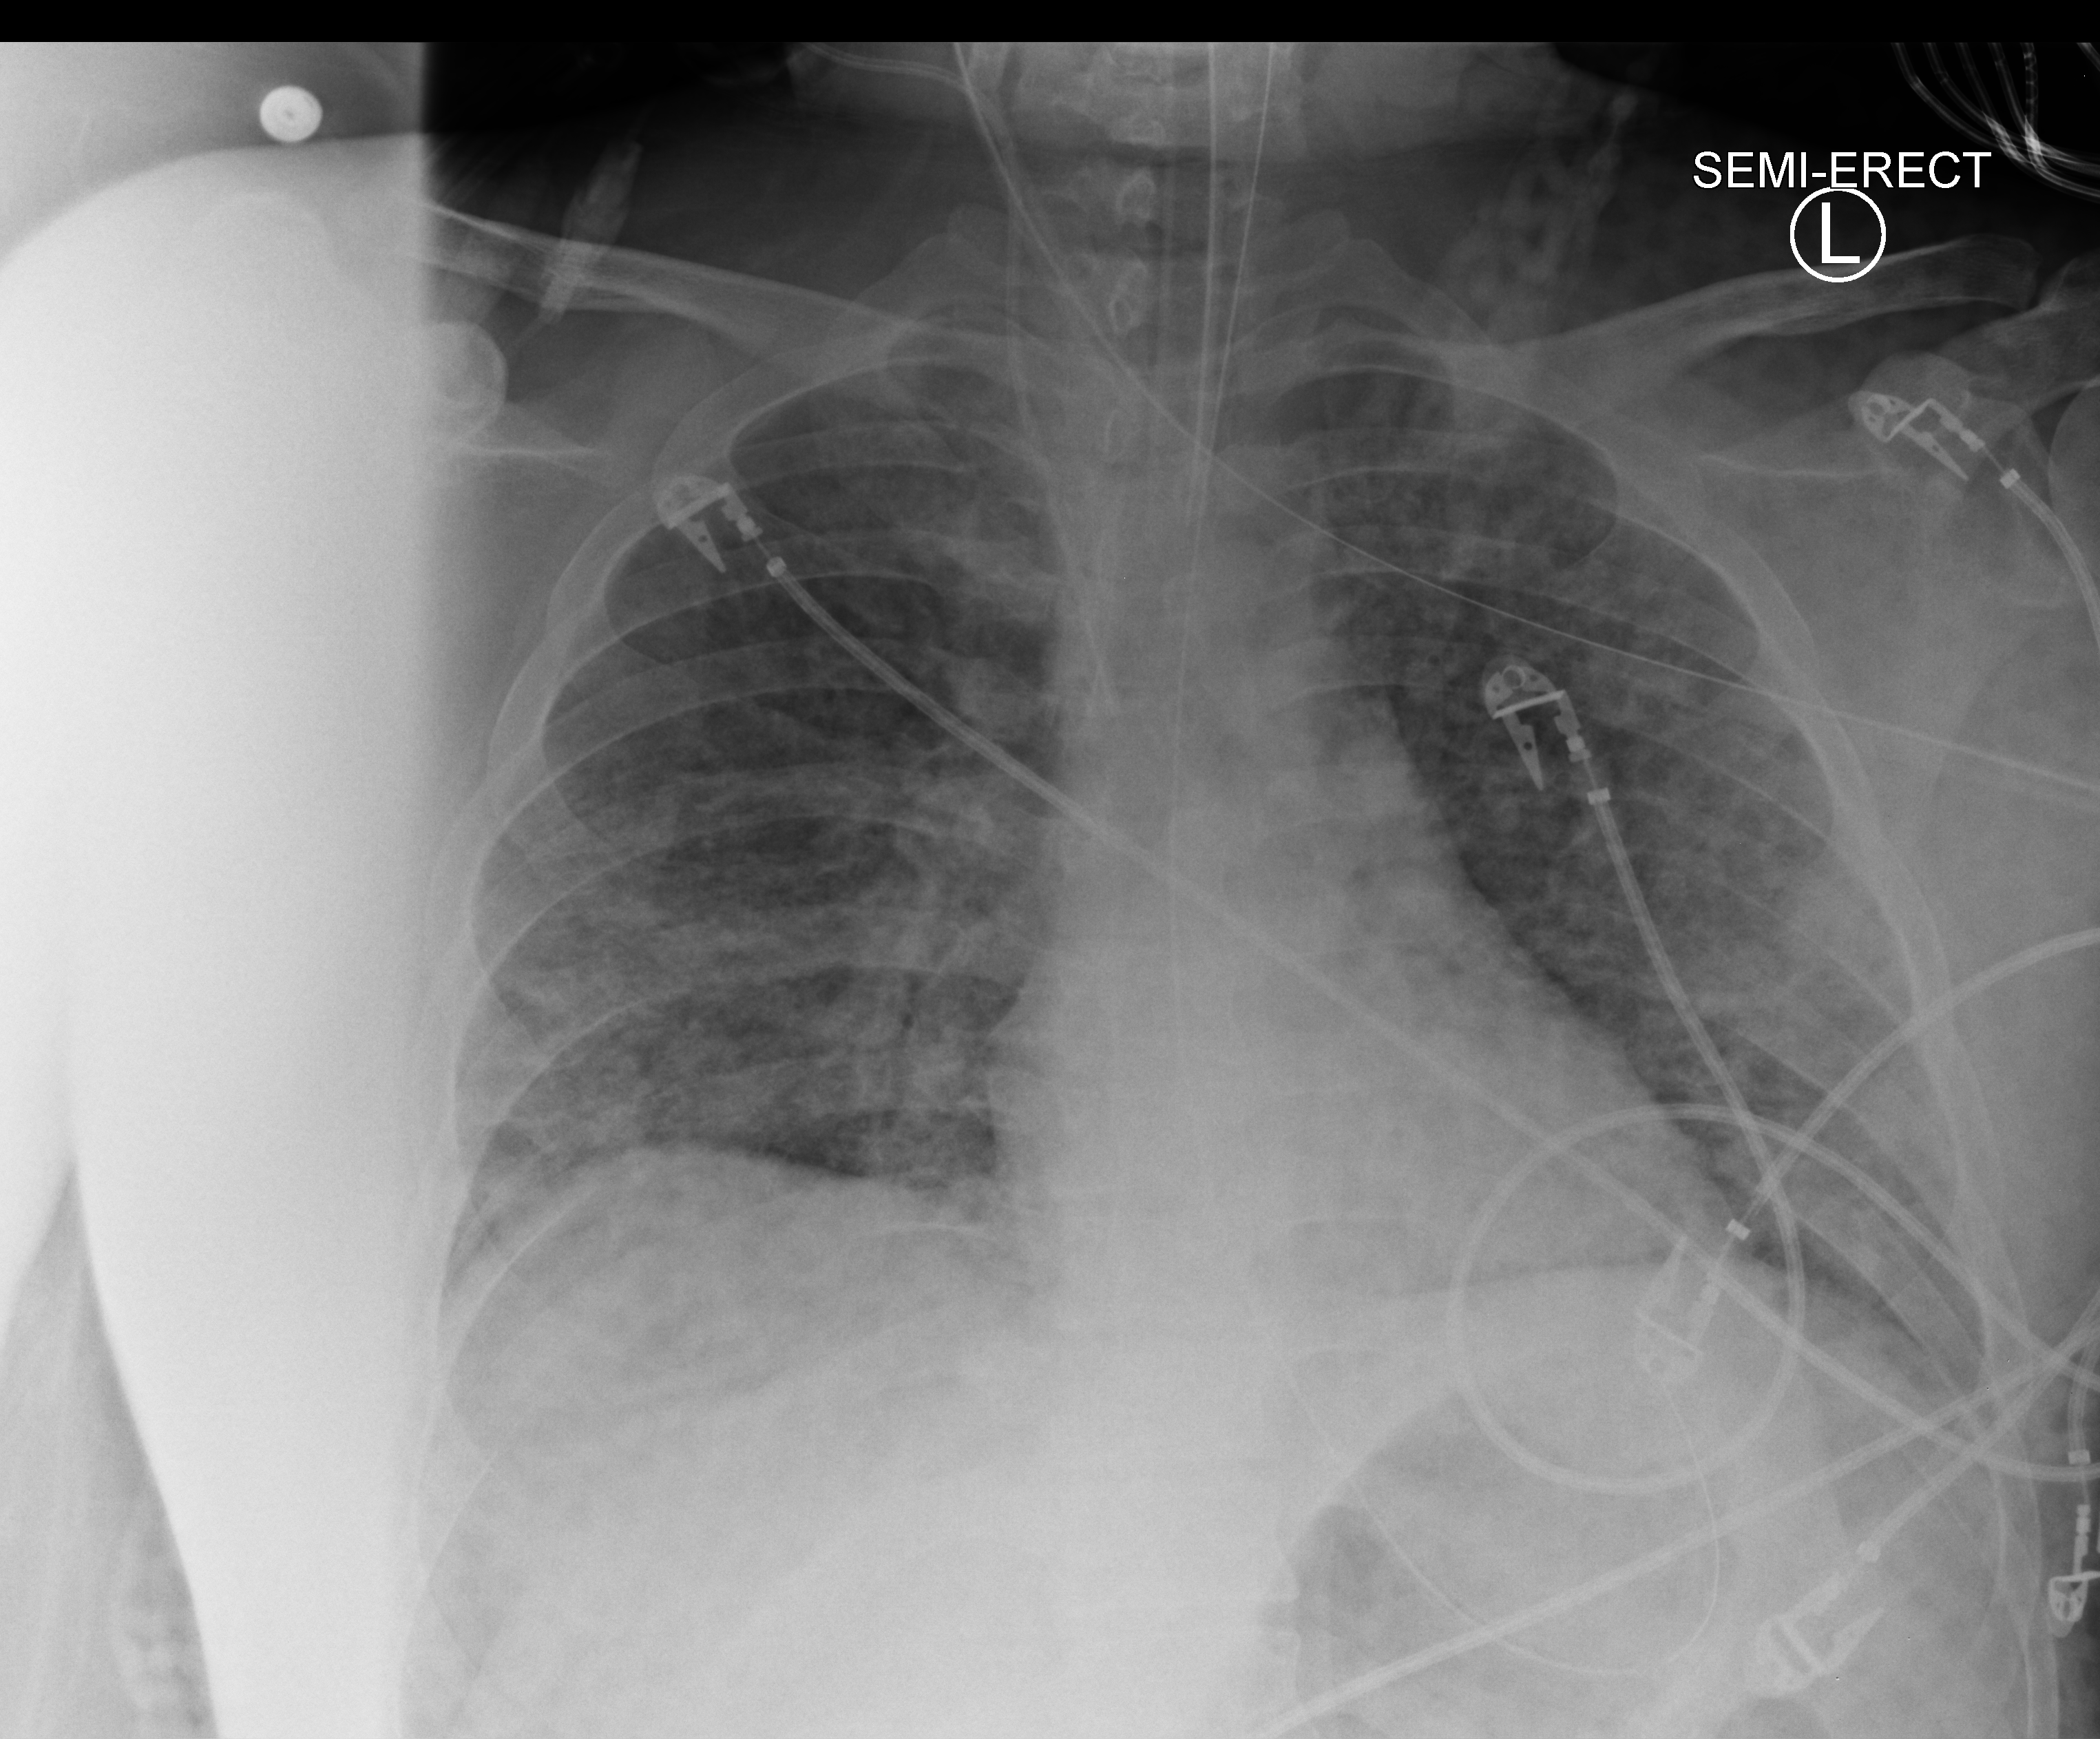
Chest X-ray (portable), anteroposterior (AP) projection. Patient hospitalised with COVID-19; male, aged 18–59 years.
Admission-level facts for this patient (not findings on this image; timing relative to this image not recorded): chronic kidney disease (admission record): no.